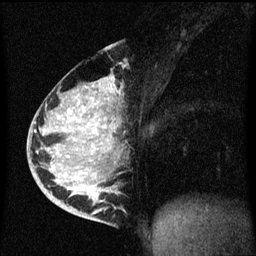
Breast MRI (dynamic contrast-enhanced), one sagittal slice; dynamic contrast-enhanced series, image 2 of 3 at this slice position (ordered by acquisition); 1.5 T; TE 4.2 ms, TR 8.4 ms; 256 × 256 image matrix. Female patient, age 34 years. Case-level facts recorded for this patient, not image findings: setting: breast cancer imaged before/during neoadjuvant chemotherapy; receptor status: HR-positive, HER2-negative.
Structures marked on this image (semi-automatically segmented with operator editing):
- analysis volume of interest (the breast-tissue region the enhancement analysis was run in; not a lesion): bounding box <34,48,123,215> (left, top, right, bottom; pixels)
- tumour enhancement mask (voxels above the 70 % enhancement threshold inside the analysis volume of interest): <52,82,113,195>